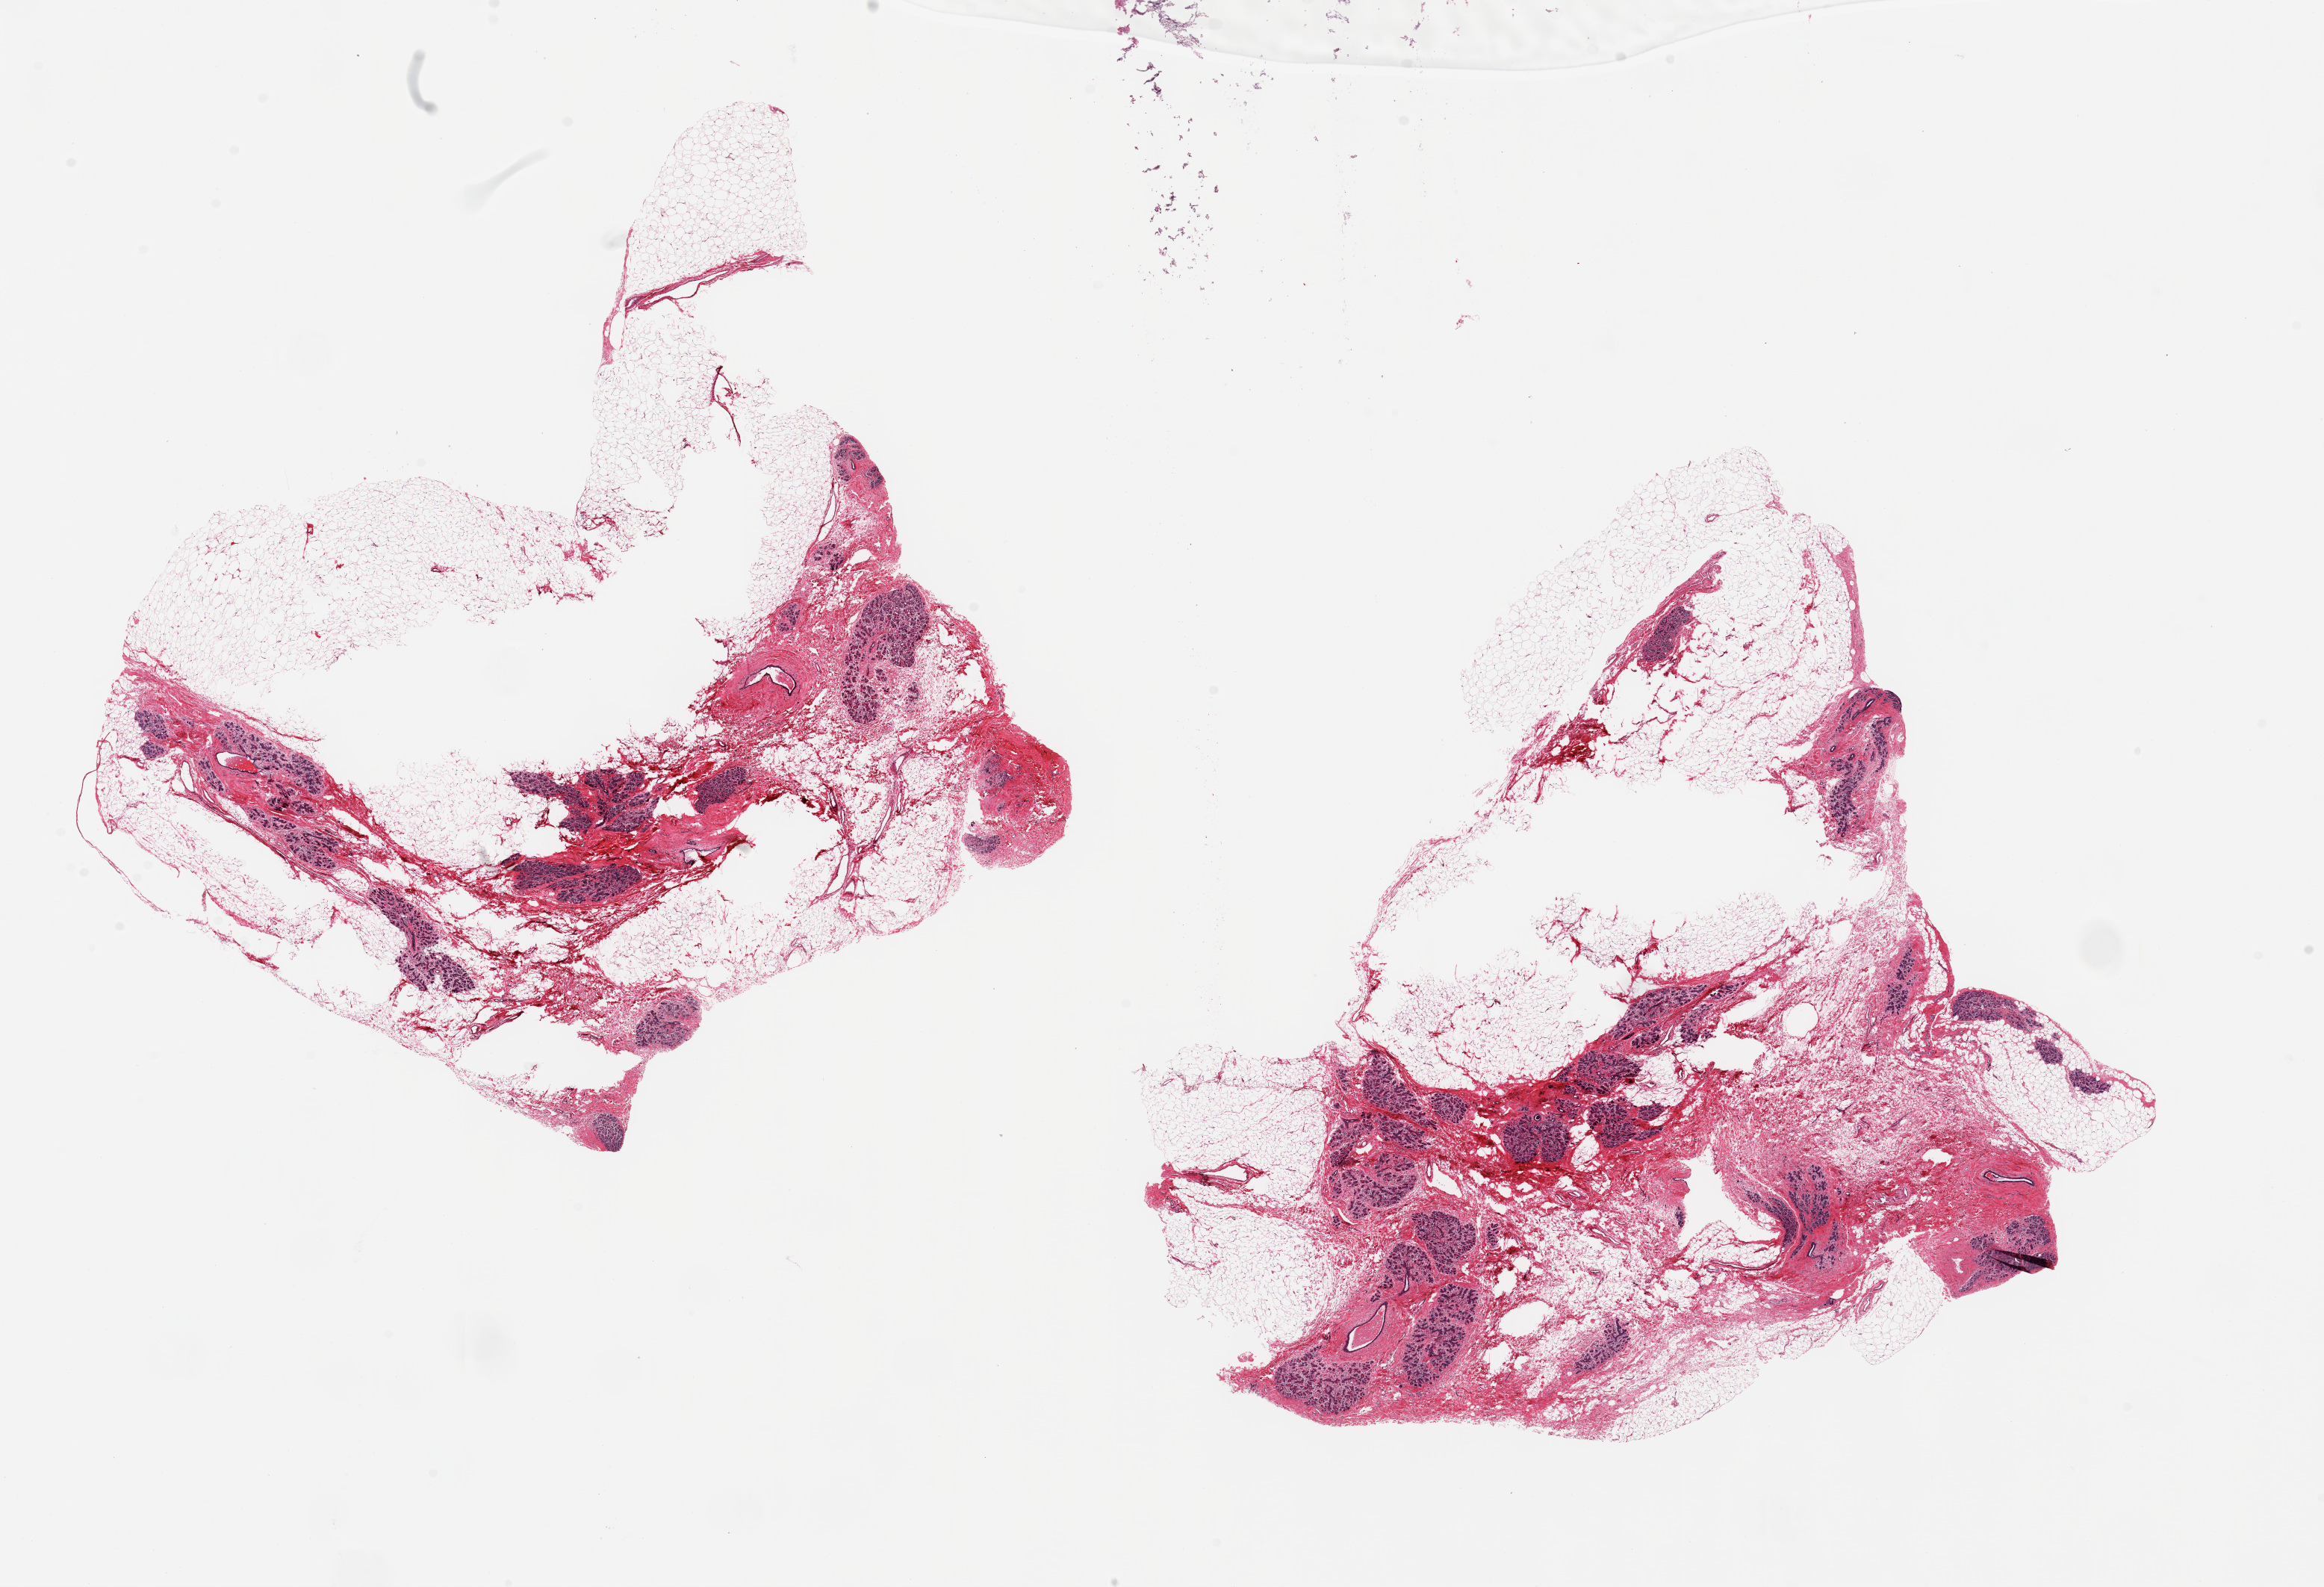
Haematoxylin and eosin whole-slide image, brightfield, whole scanned area (about 24.6 x 16.8 mm, from a 20x scan) shown as a low-resolution overview; PAXgene-fixed paraffin-embedded (PFPE) section; section of breast (target tissue); donor tissue sample. Female donor.
Pathologist's review note for this sample: 2 pieces, 11x10 & 10x10 mm; 50 & 70% adipose tissue; abundant lobular and ductal components; unfixed central areas in adipose tissue.